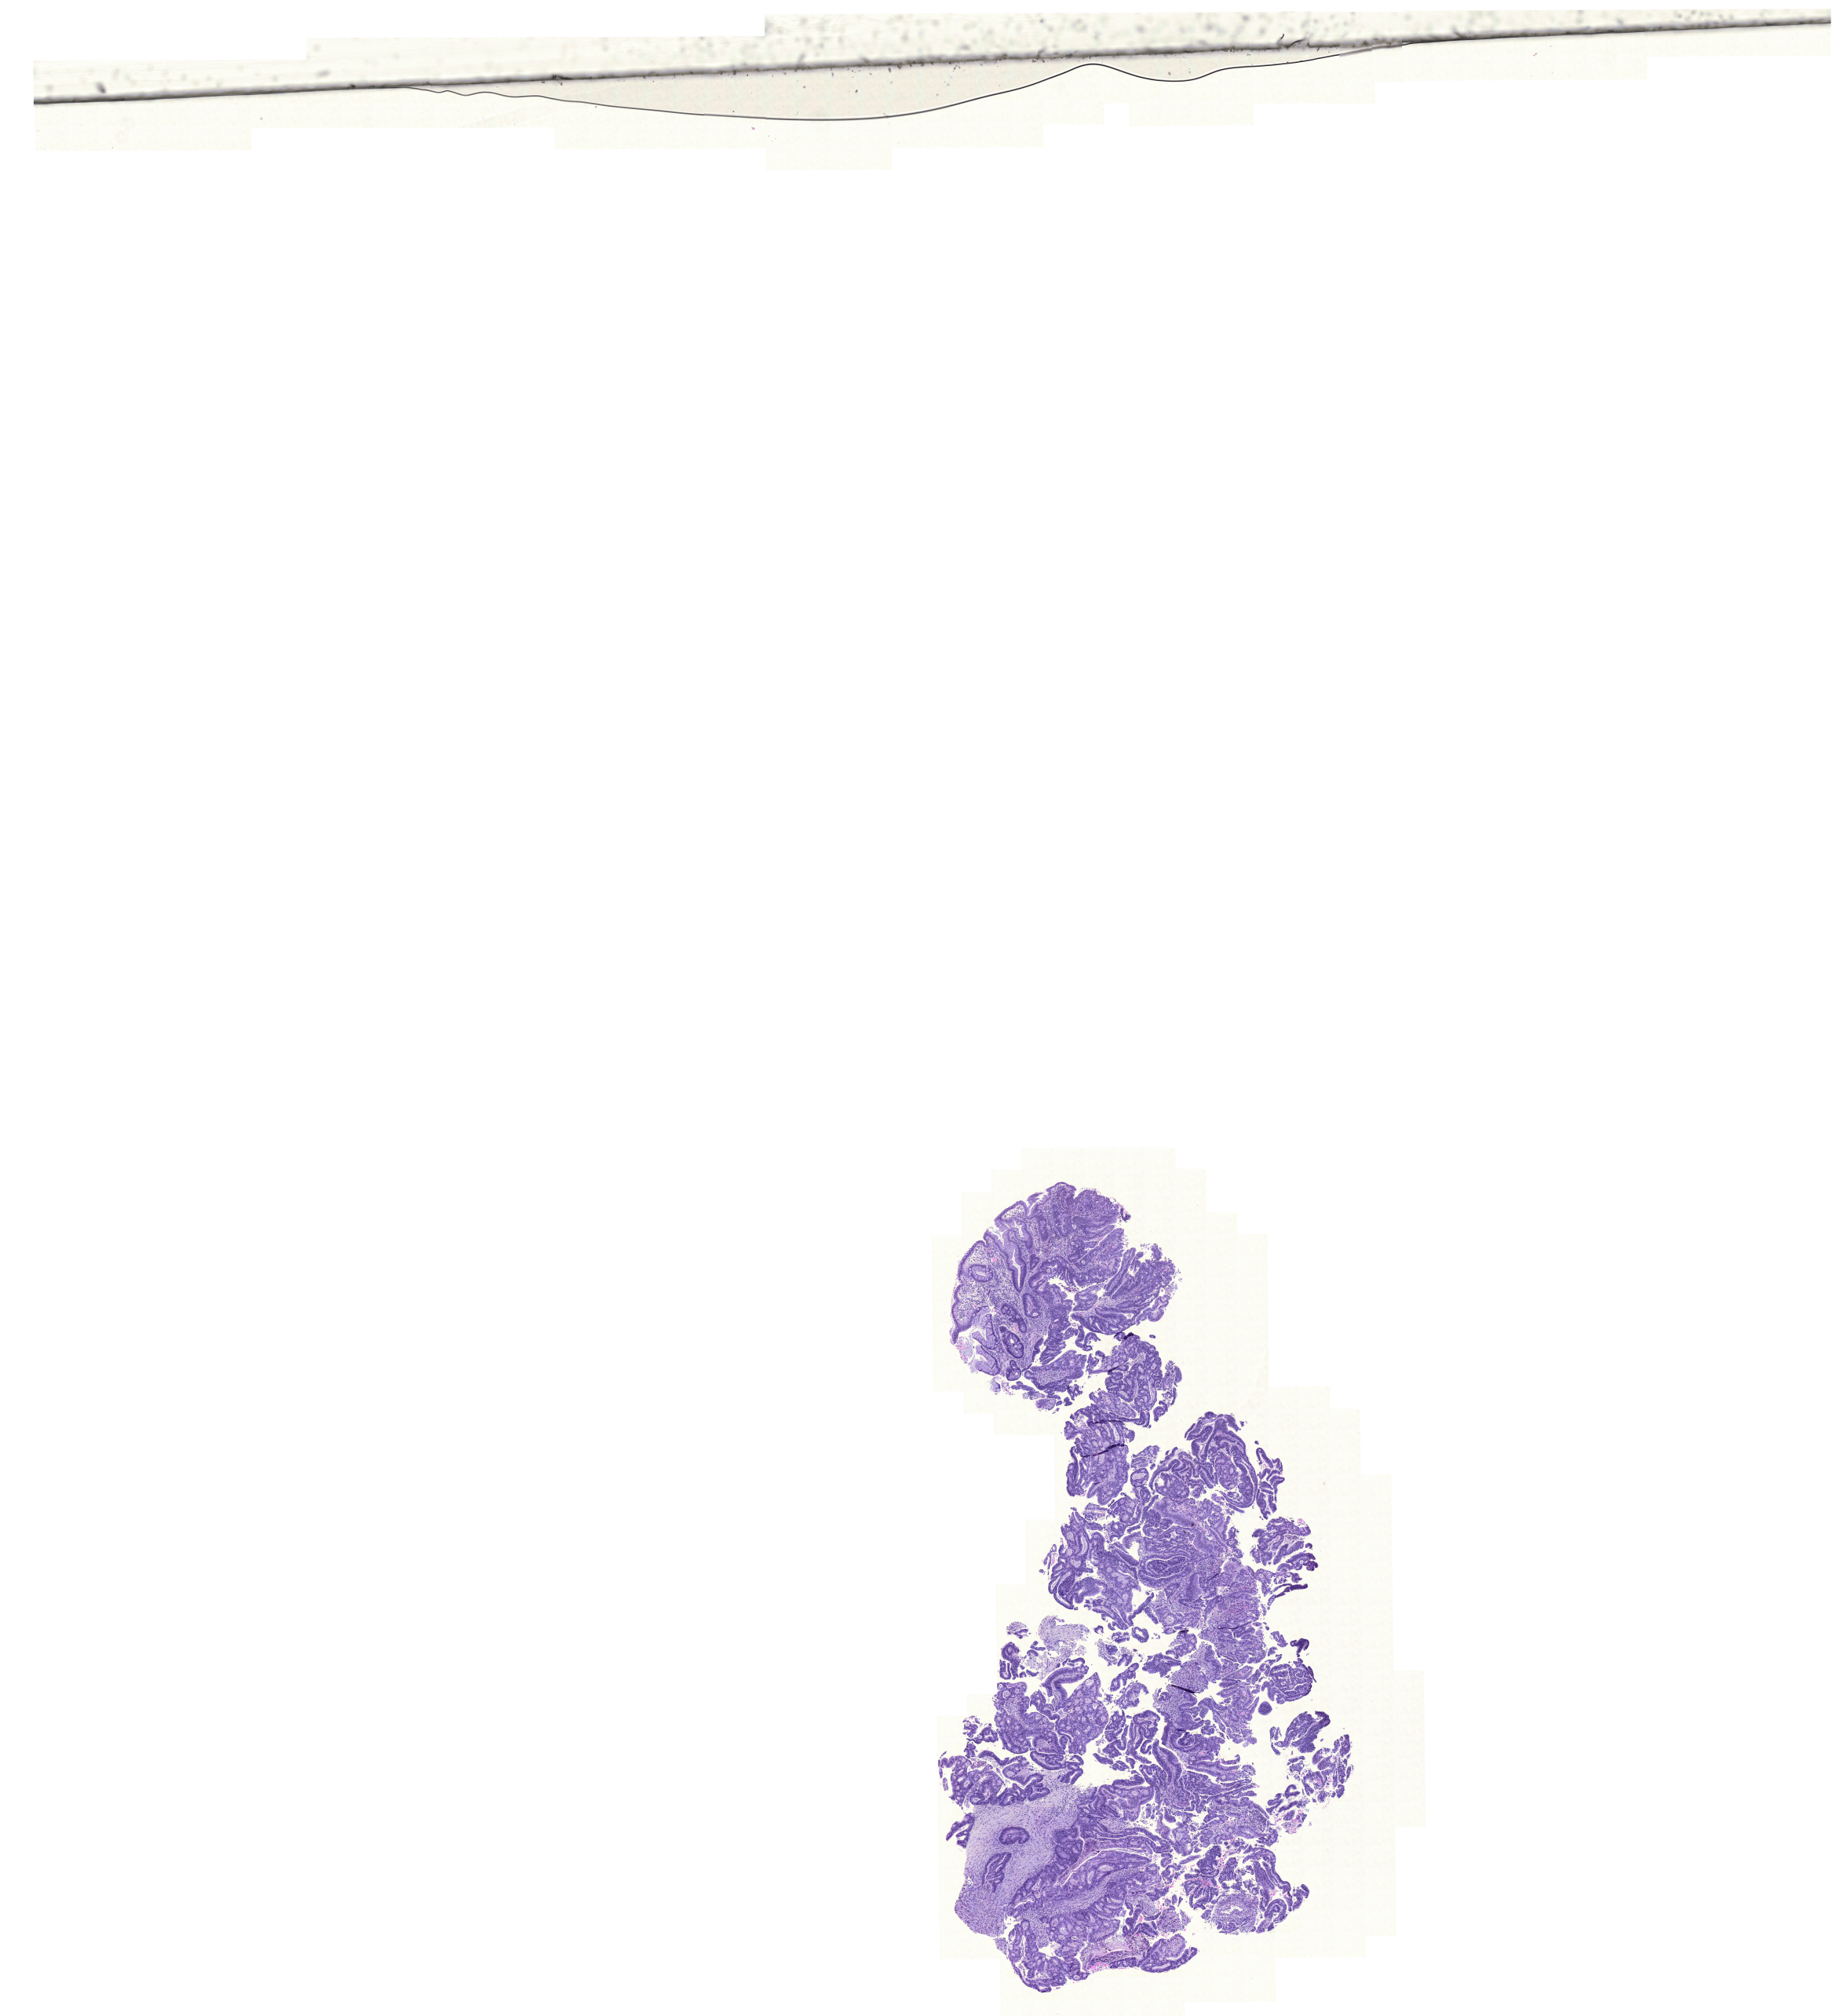
Digitized Hematoxylin and eosin (H&E) stained tissue section (whole slide), shown as a low-resolution overview of the whole scanned area (about 17.4 x 19.1 mm), FFPE section, rectum, primary tumour sample. Patient: female, age at initial diagnosis 59 years.
Pathologic diagnosis: Adenocarcinoma, NOS.